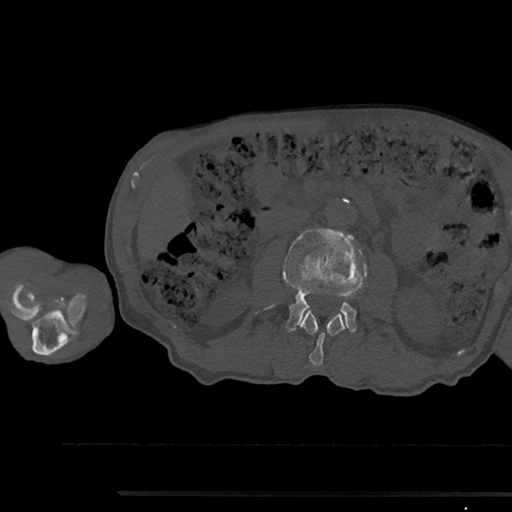
CT including the spine, one axial slice; reconstruction kernel Br40s/3; 120 kVp; bone window (W 1800 / L 400 HU); 0.5 mm slice thickness; 512 × 512 image matrix, field of view 367 × 367 mm. Male patient, age 79 years. Case-level facts recorded for this patient, not image findings: primary cancer: prostate.
Annotated regions visible in this slice (semi-automatic segmentation, software-assisted and operator-edited):
- L2 vertebra: bounding box <299,310,345,366> (left, top, right, bottom; pixels)
- L3 vertebra: <270,229,368,332>